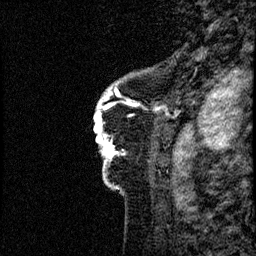
Breast MRI (dynamic contrast-enhanced), one sagittal slice; position 7 of 60 along the scan axis; dynamic contrast-enhanced study with each time point stored as its own series, time point 2 of 4 at this slice position (early post-contrast, ordered by acquisition time); 1.5 T; TE 4.2 ms, TR 17.6 ms; 2 mm slice thickness; 256 × 256 image matrix. Female patient, age 40 years. From the clinical record (not read from this slice): setting: breast cancer imaged before/during neoadjuvant chemotherapy; receptor status: HER2-positive.
Outlined on this slice (semi-automatically segmented with operator editing):
- analysis volume of interest (the breast-tissue region the enhancement analysis was run in; not a lesion): bounding box <91,55,185,206> (left, top, right, bottom; pixels)
- tumour enhancement mask (voxels above the 100 % enhancement threshold inside the analysis volume of interest): <94,87,161,170>